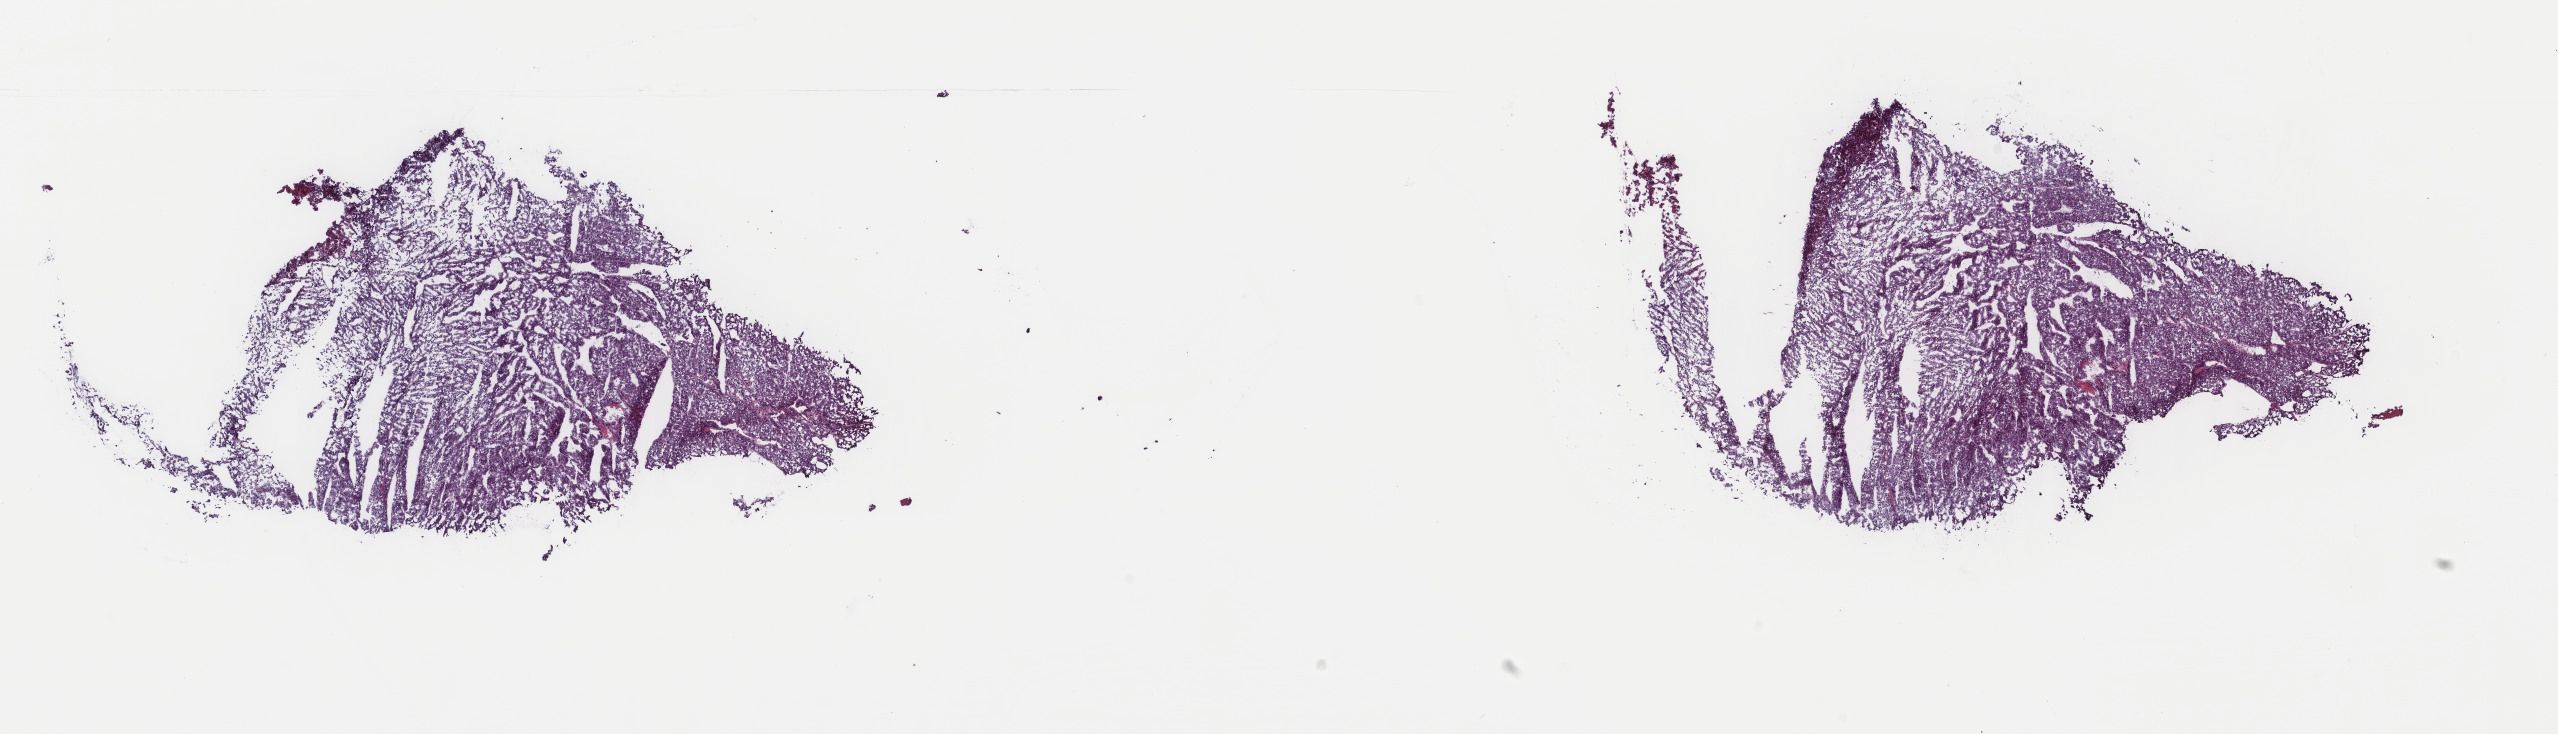
Digitized H&E-stained tissue section (whole slide), whole scanned area (about 20.3 x 5.8 mm, slide scanned at 40x) shown as a low-resolution overview; frozen section from the top of the tissue portion; sample: primary tumour, adrenal cortex. Female, age 55 years at initial diagnosis. Pathologist review of this section (percent, as recorded): tumour cells 95%, tumour nuclei 100%.
Pathologic diagnosis: Adrenal cortical carcinoma (cortex of adrenal gland).